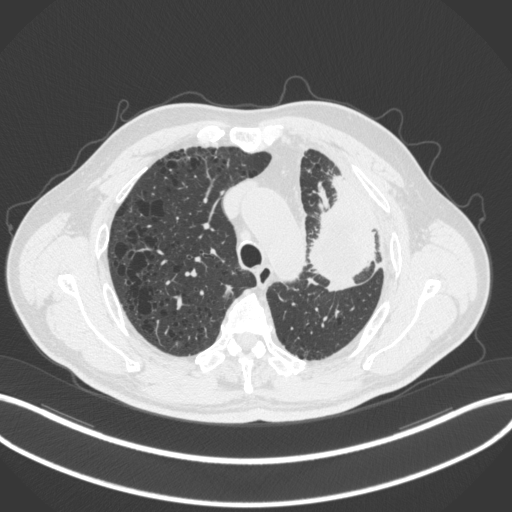
Chest CT, one axial slice. Position 223 of 286 along the scan axis. 120 kVp. Lung window (W 1500 / L -600 HU). 1 mm slice thickness. 512 × 512 image matrix. Male patient, age 68 years. From the clinical record (not read from this slice): clinical TNM (as recorded): T3 N3 M1.
Structures marked on this image (rectangle marked by the reading radiologist):
- lung tumour (recorded histology: adenocarcinoma): box from (x=309, y=171) to (x=383, y=294) px